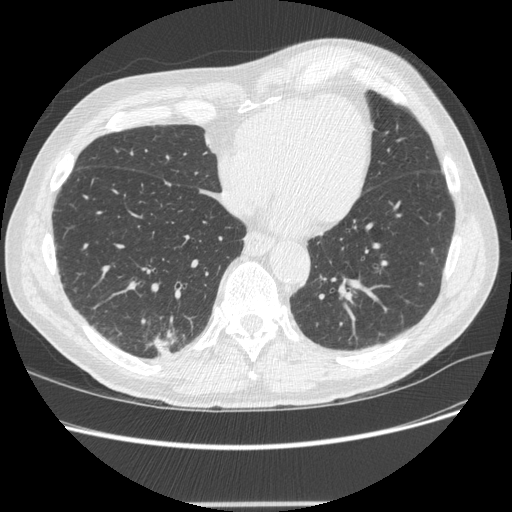
Low-dose screening chest CT, one axial slice. Position 76 of 245 along the scan axis. 120 kVp. Lung window (W 1500 / L -600 HU). 512 × 512 image matrix, field of view 372 × 372 mm.
Outlined on this slice (expert manual segmentation):
- lesion 1 (tumor, lower lobe of right lung): box from (x=151, y=330) to (x=177, y=356) px